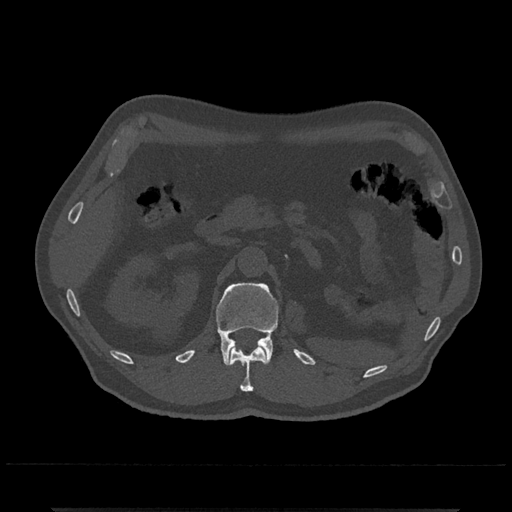
CT including the spine, one axial slice. Slice 386 of 797 in the series (ordered by position). 120 kVp. Bone window (W 1800 / L 400 HU). 512 × 512 image matrix, field of view 393 × 393 mm. Male patient, age 67 years. From the clinical record (not read from this slice): primary cancer: prostate.
Structures marked on this image (semi-automatic segmentation, software-assisted and operator-edited):
- L1 vertebra: bounding box <216,282,279,365> (left, top, right, bottom; pixels)
- T12 vertebra: <230,346,267,392>